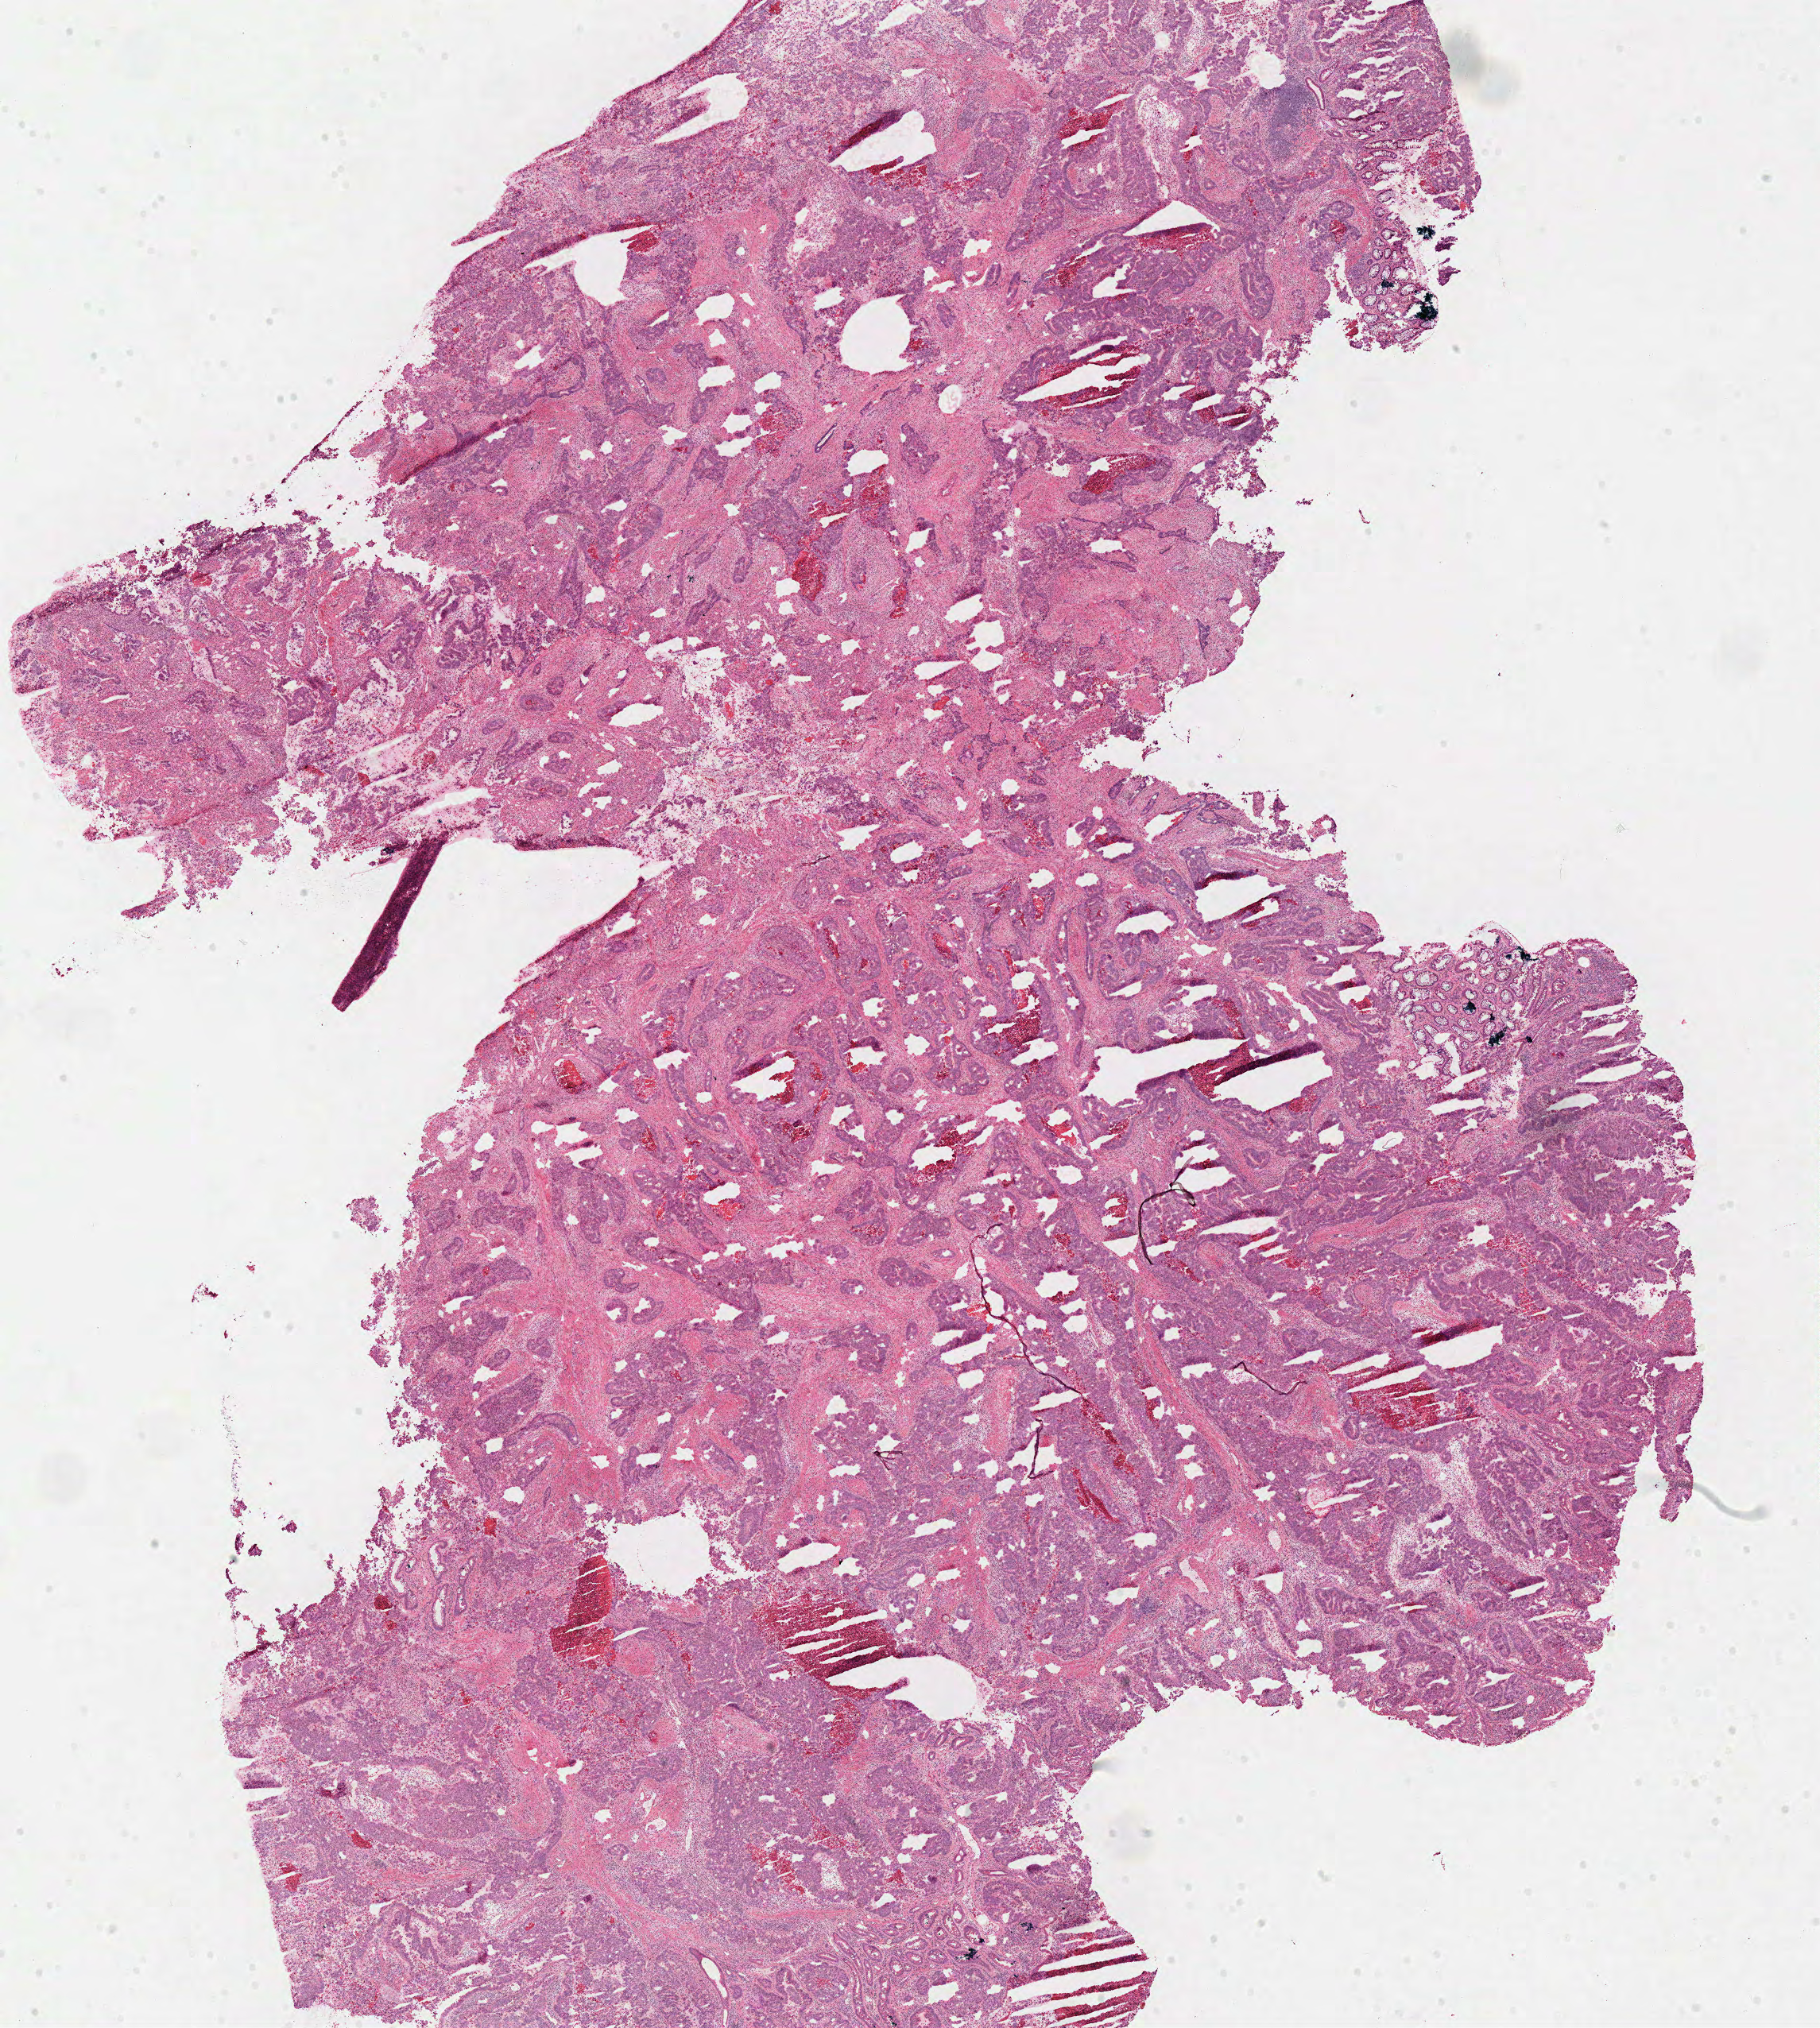
H&E-stained whole-slide image — low-resolution overview of the scanned area, about 18.0 x 20.1 mm (slide scanned at 40x). Frozen section from the top of the tissue portion. Sample: primary tumour, rectum. Patient: female, age at initial diagnosis 62 years. Pathologist review of this section (percent, as recorded): tumour cells 94%, tumour nuclei 80%, normal cells 1%, stromal cells 0%, necrosis 5%. Infiltration values recorded for this section: lymphocyte infiltration 15%, monocyte infiltration 1%, neutrophil infiltration 2%.
* lymph nodes positive (case pathology): 1 of 19 examined
* diagnosis: Adenocarcinoma, NOS
* AJCC pathologic stage: IIIB